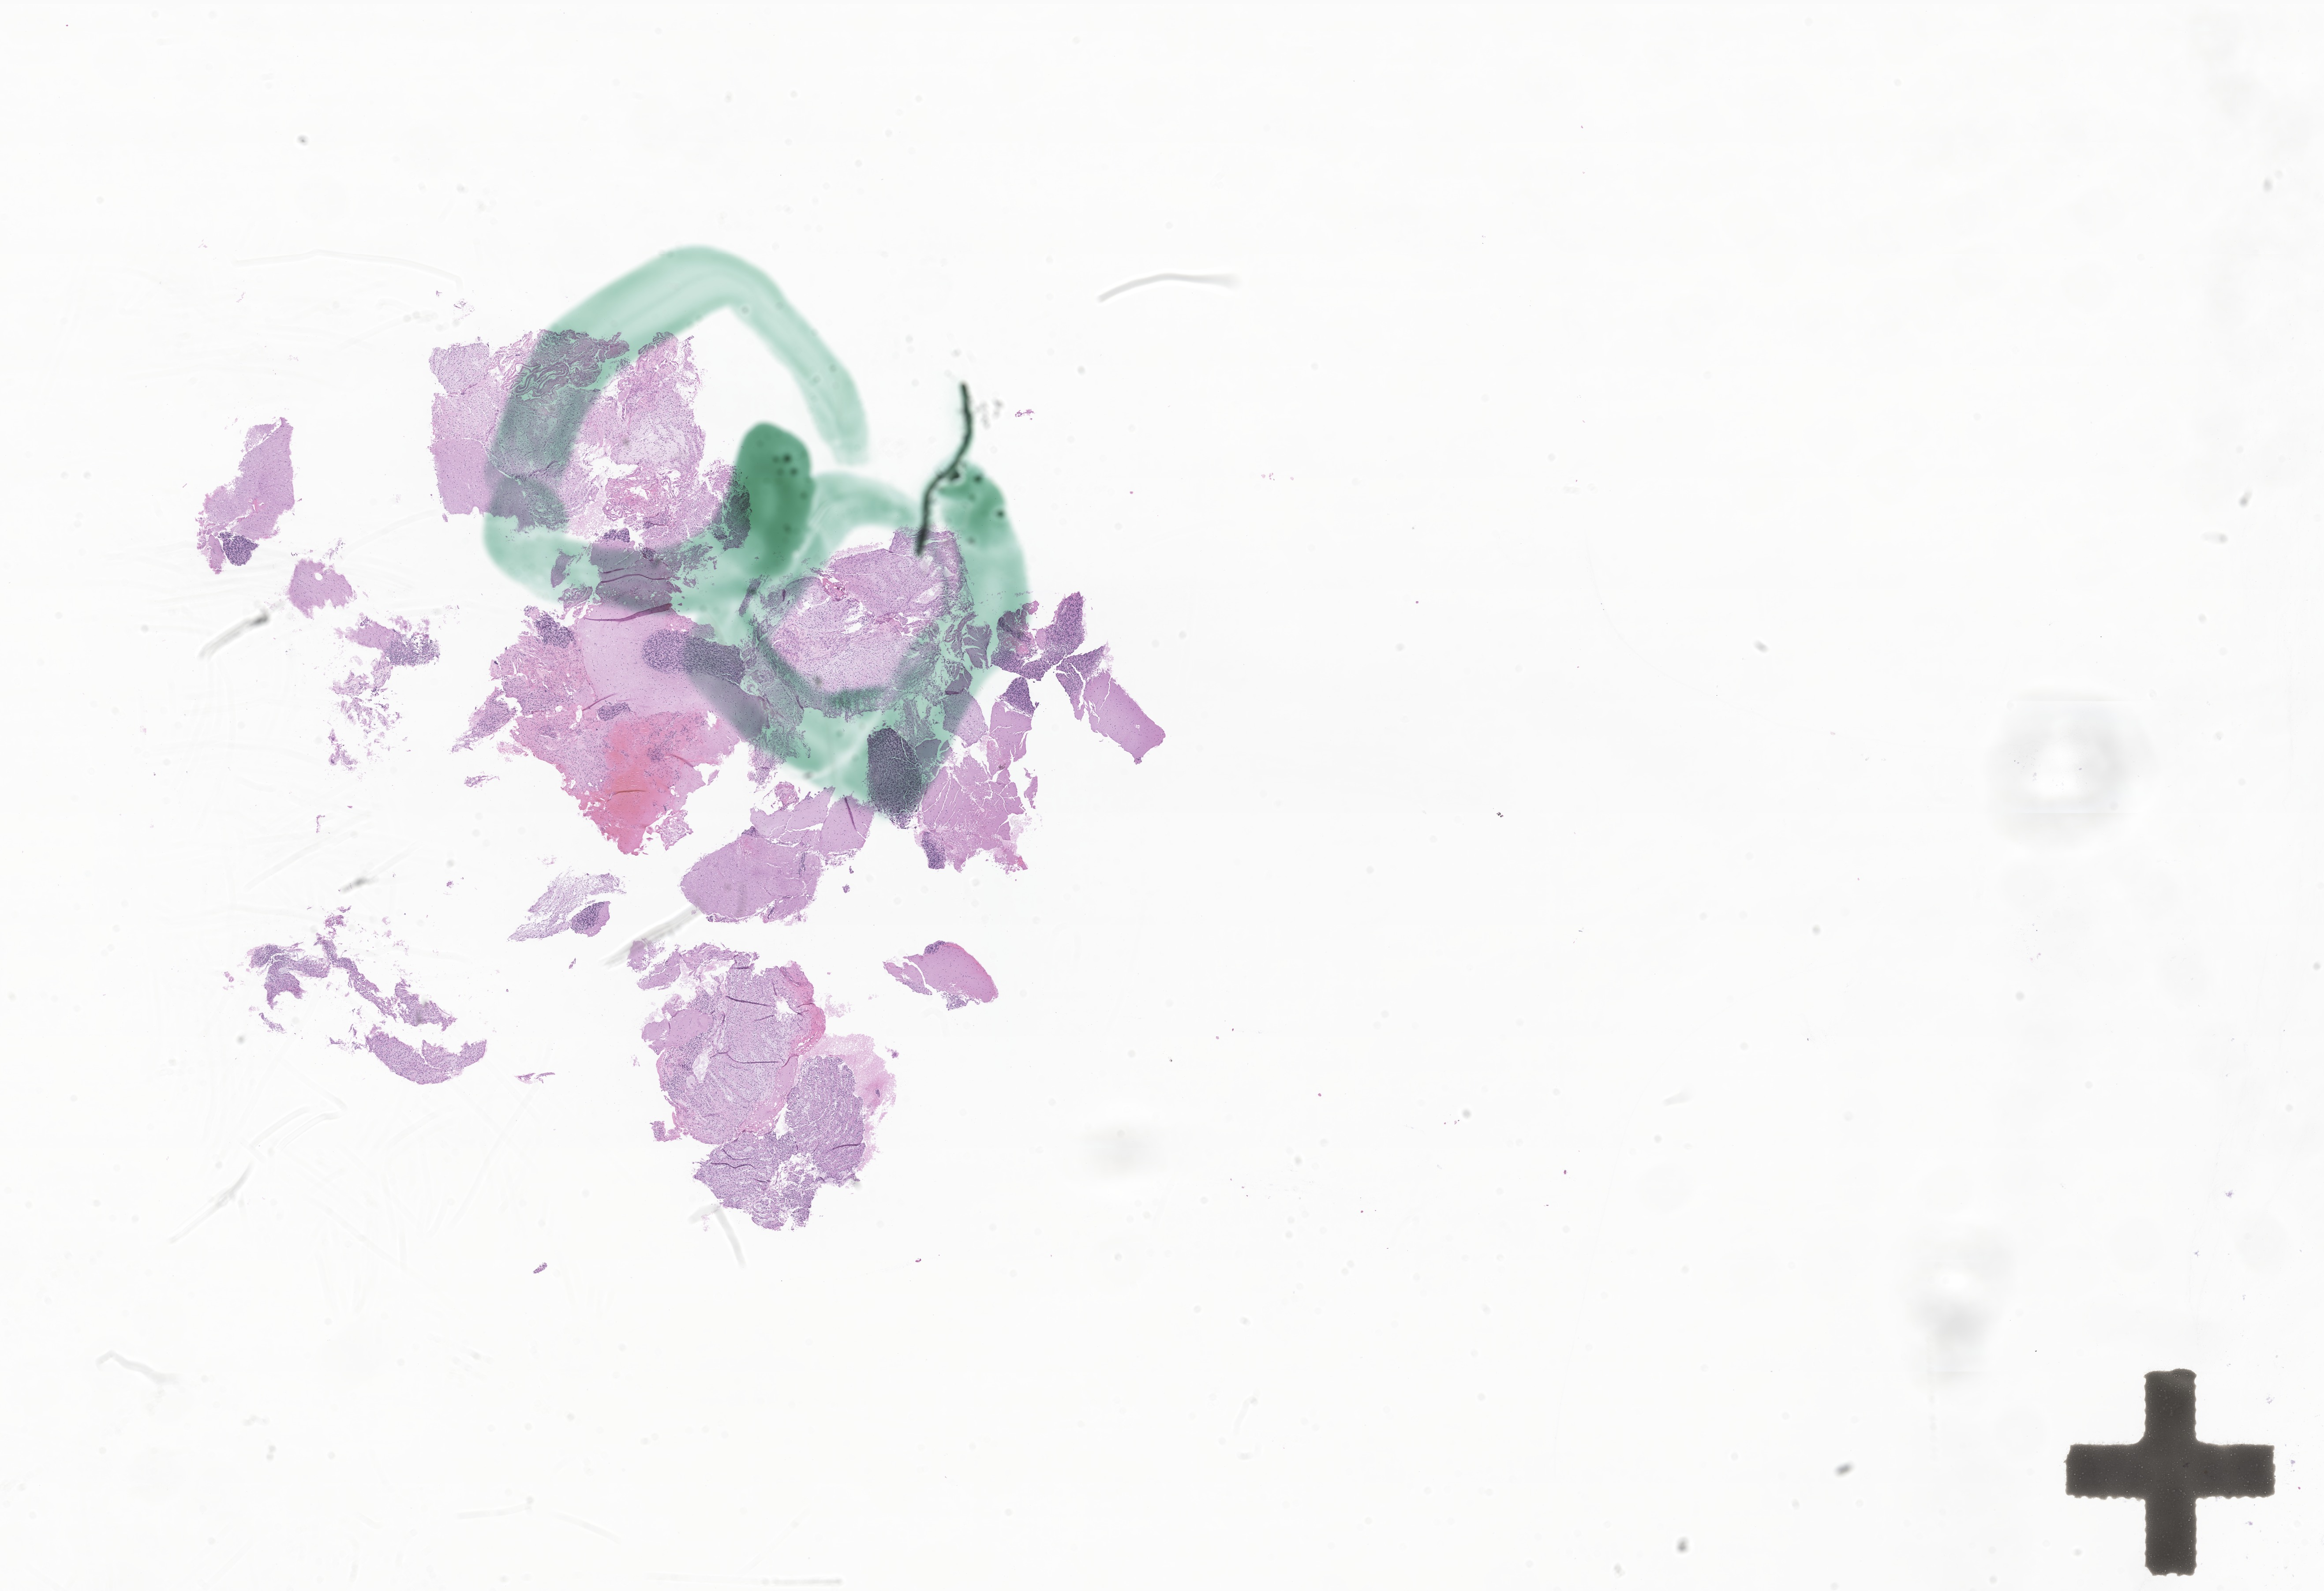
Digitized hematoxylin and eosin (H&E)-stained section of tumor tissue from the cerebellum — shown as a low-resolution overview of the whole scanned area (about 22.2 x 15.2 mm), FFPE section. Patient male; age 136 months (11 years 4 months).
• recorded diagnosis: Astrocytoma, NOS